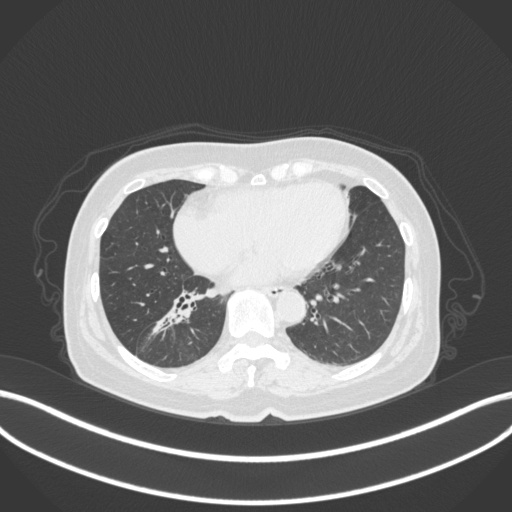
Chest CT, one axial slice. Slice 152 of 429 in the series (ordered by position). Reconstruction kernel B31f. 120 kVp. Lung window (W 1500 / L -600 HU). 1 mm slice thickness. 512 × 512 image matrix, field of view 400 × 400 mm. Female patient, age 67 years. From the clinical record (not read from this slice): clinical TNM (as recorded): T1c N1 M0; histopathological grade: G2-3.
Outlined on this slice (rectangle marked by the reading radiologist):
- lung tumour (recorded histology: adenocarcinoma): bounding box (x1, y1, x2, y2) in pixels: (150, 295, 199, 339)